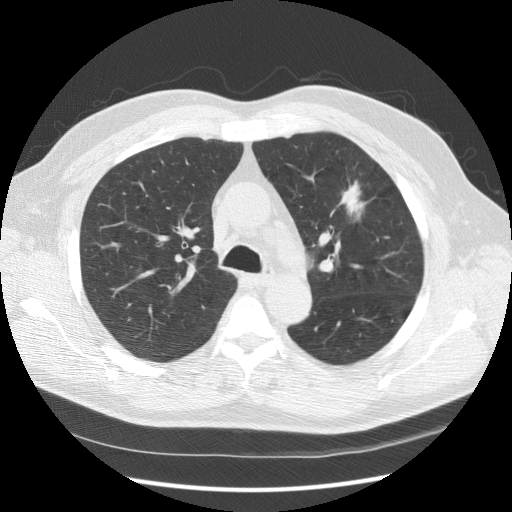
Low-dose screening chest CT, one axial slice; slice 106 of 157 in the series (ordered by position); 120 kVp; lung window (W 1500 / L -600 HU); 2.5 mm slice thickness; 512 × 512 image matrix, field of view 370 × 370 mm.
Structures marked on this image (outlined manually by an expert reader):
- lesion 1 (tumor, upper lobe of left lung): bounding box <341,182,366,220> (left, top, right, bottom; pixels)